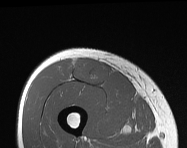
MRI of an extremity soft-tissue mass, one axial slice. Slice 54 of 114 in the series (ordered by position). MR volume resampled by the dataset authors to the PET/CT grid (not the native acquisition matrix). 3.27 mm slice thickness. 187 × 148 image matrix. Male patient. From the clinical record (not read from this slice): histological type: pleiomorphic leiomyosarcoma; grade: intermediate; site of the primary tumour: right thigh.
Outlined on this slice (expert contour drawn on MRI and transferred to this co-registered scan by the dataset authors):
- gross tumour volume including surrounding oedema: box from (x=73, y=58) to (x=112, y=85) px